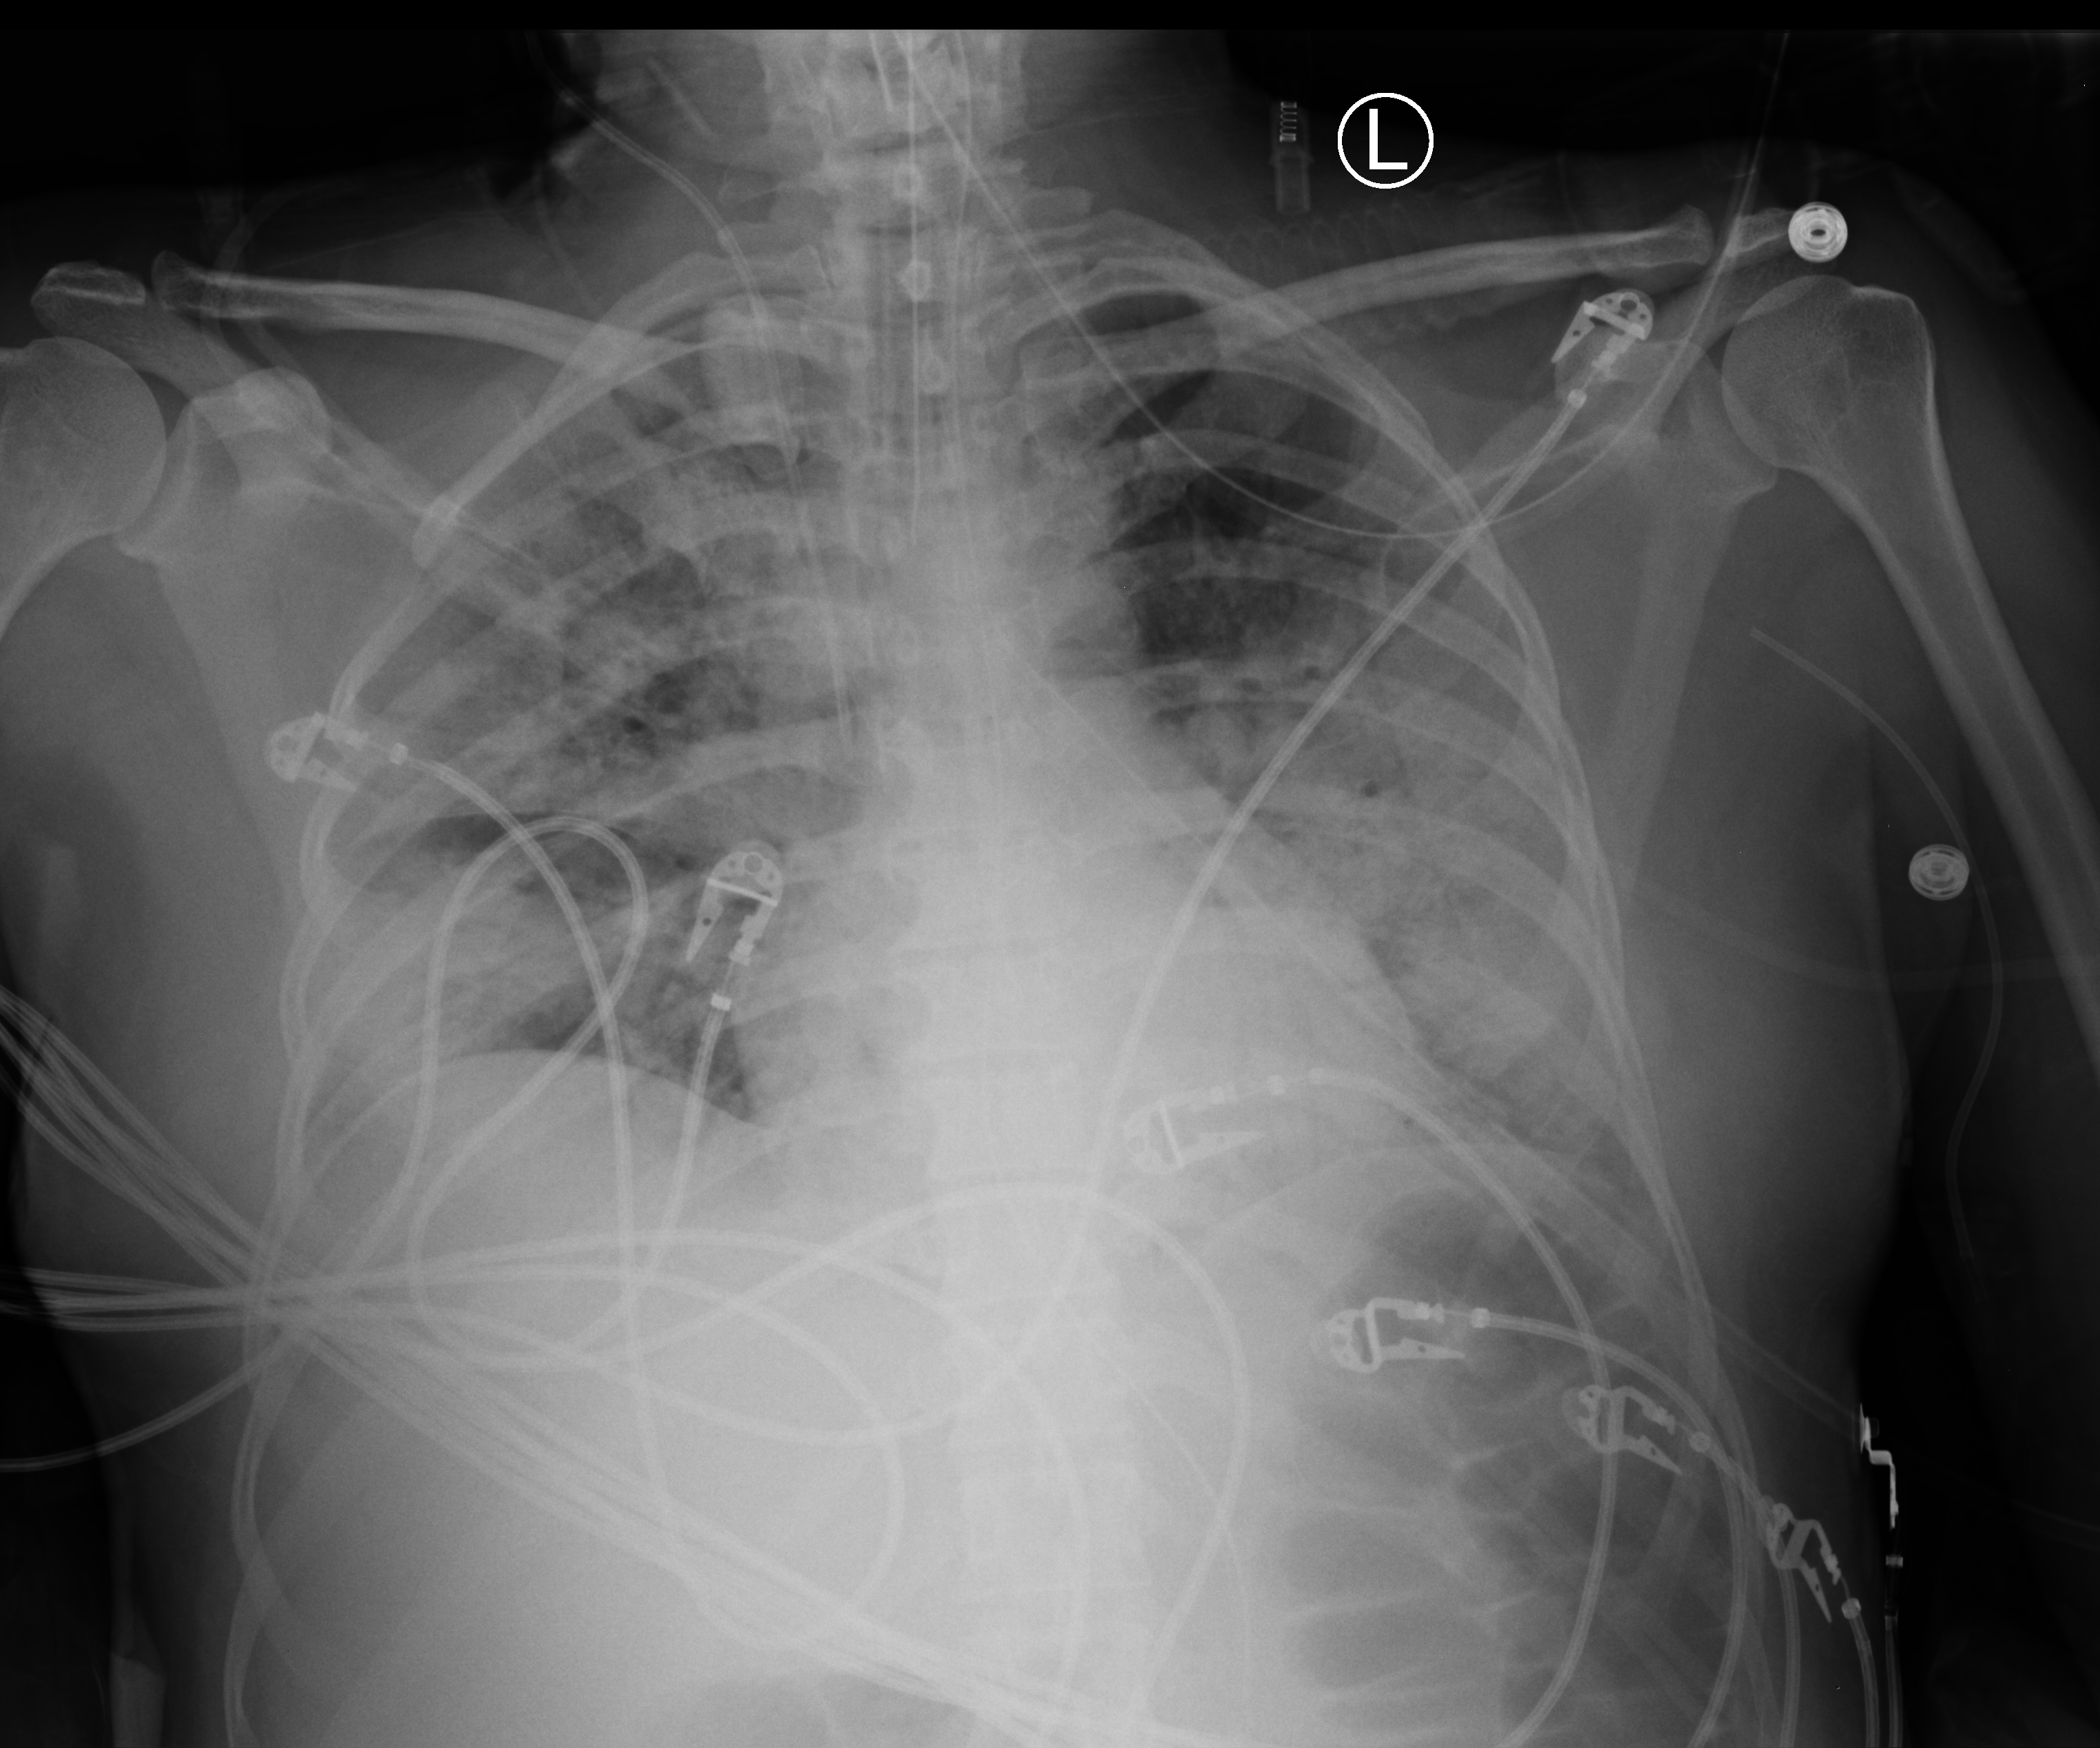
Portable chest radiograph. Patient hospitalised with COVID-19; female, aged 18–59 years.
From the hospital-stay record, not from the radiograph (when in the stay this image was taken is not recorded): hypertension (admission record): no; diabetes (admission record): no.